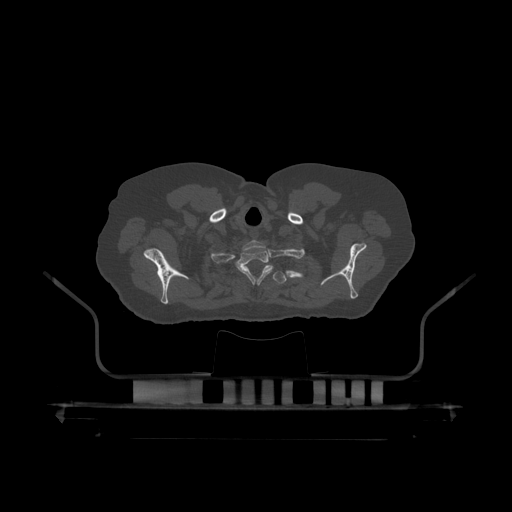
CT including the spine, one axial slice; reconstruction kernel STANDARD; 120 kVp; bone window (W 1800 / L 400 HU); 1.25 mm slice thickness; 512 × 512 image matrix. Patient: male, 60 years. Case-level facts recorded for this patient, not image findings: primary cancer: prostate.
Structures marked on this image (semi-automatically segmented with operator editing):
- T1 vertebra: bounding box (x1, y1, x2, y2) in pixels: (239, 241, 274, 284)
- T2 vertebra: (229, 266, 287, 284)